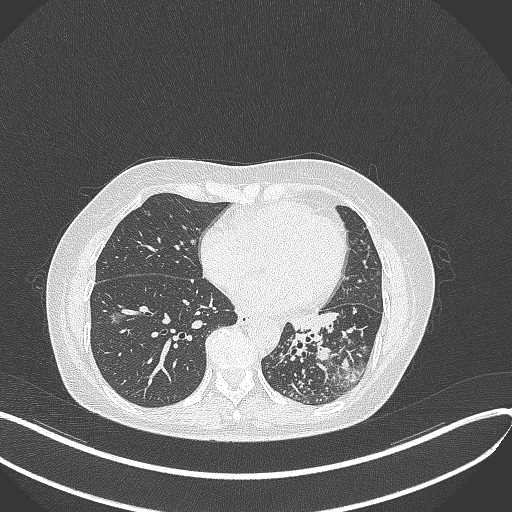
Chest CT, one axial slice. Slice 156 of 429 in the series (ordered by position). Reconstruction kernel B70f. Lung window (W 1500 / L -600 HU). 1 mm slice thickness. 512 × 512 image matrix, field of view 400 × 400 mm. Female patient, age 63 years. From the clinical record (not read from this slice): clinical TNM (as recorded): T1b N0 M0; histopathological grade: G2-3.
Outlined on this slice (bounding box drawn by a radiologist):
- lung tumour (recorded histology: adenocarcinoma): bounding box (x1, y1, x2, y2) in pixels: (280, 304, 336, 350)